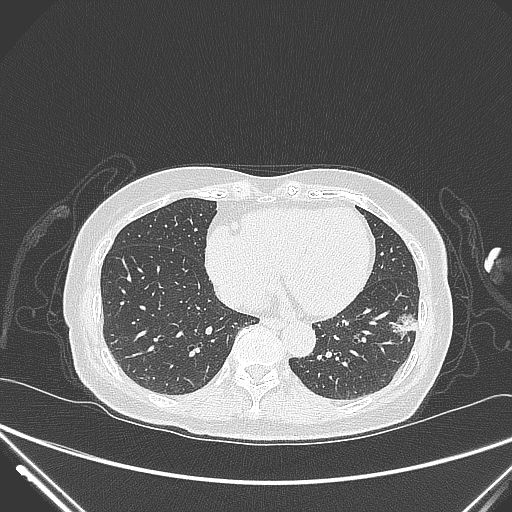
Chest CT, one axial slice. Slice 105 of 310 in the series (ordered by position). 120 kVp. Lung window (W 1500 / L -600 HU). 1 mm slice thickness. 512 × 512 image matrix, field of view 377 × 377 mm. Patient: female, 82 years. Case-level facts recorded for this patient, not image findings: clinical TNM (as recorded): T1c N0 M0; histopathological grade: G2.
Outlined on this slice (bounding box drawn by a radiologist):
- lung tumour (recorded histology: adenocarcinoma): box from (x=382, y=301) to (x=424, y=351) px